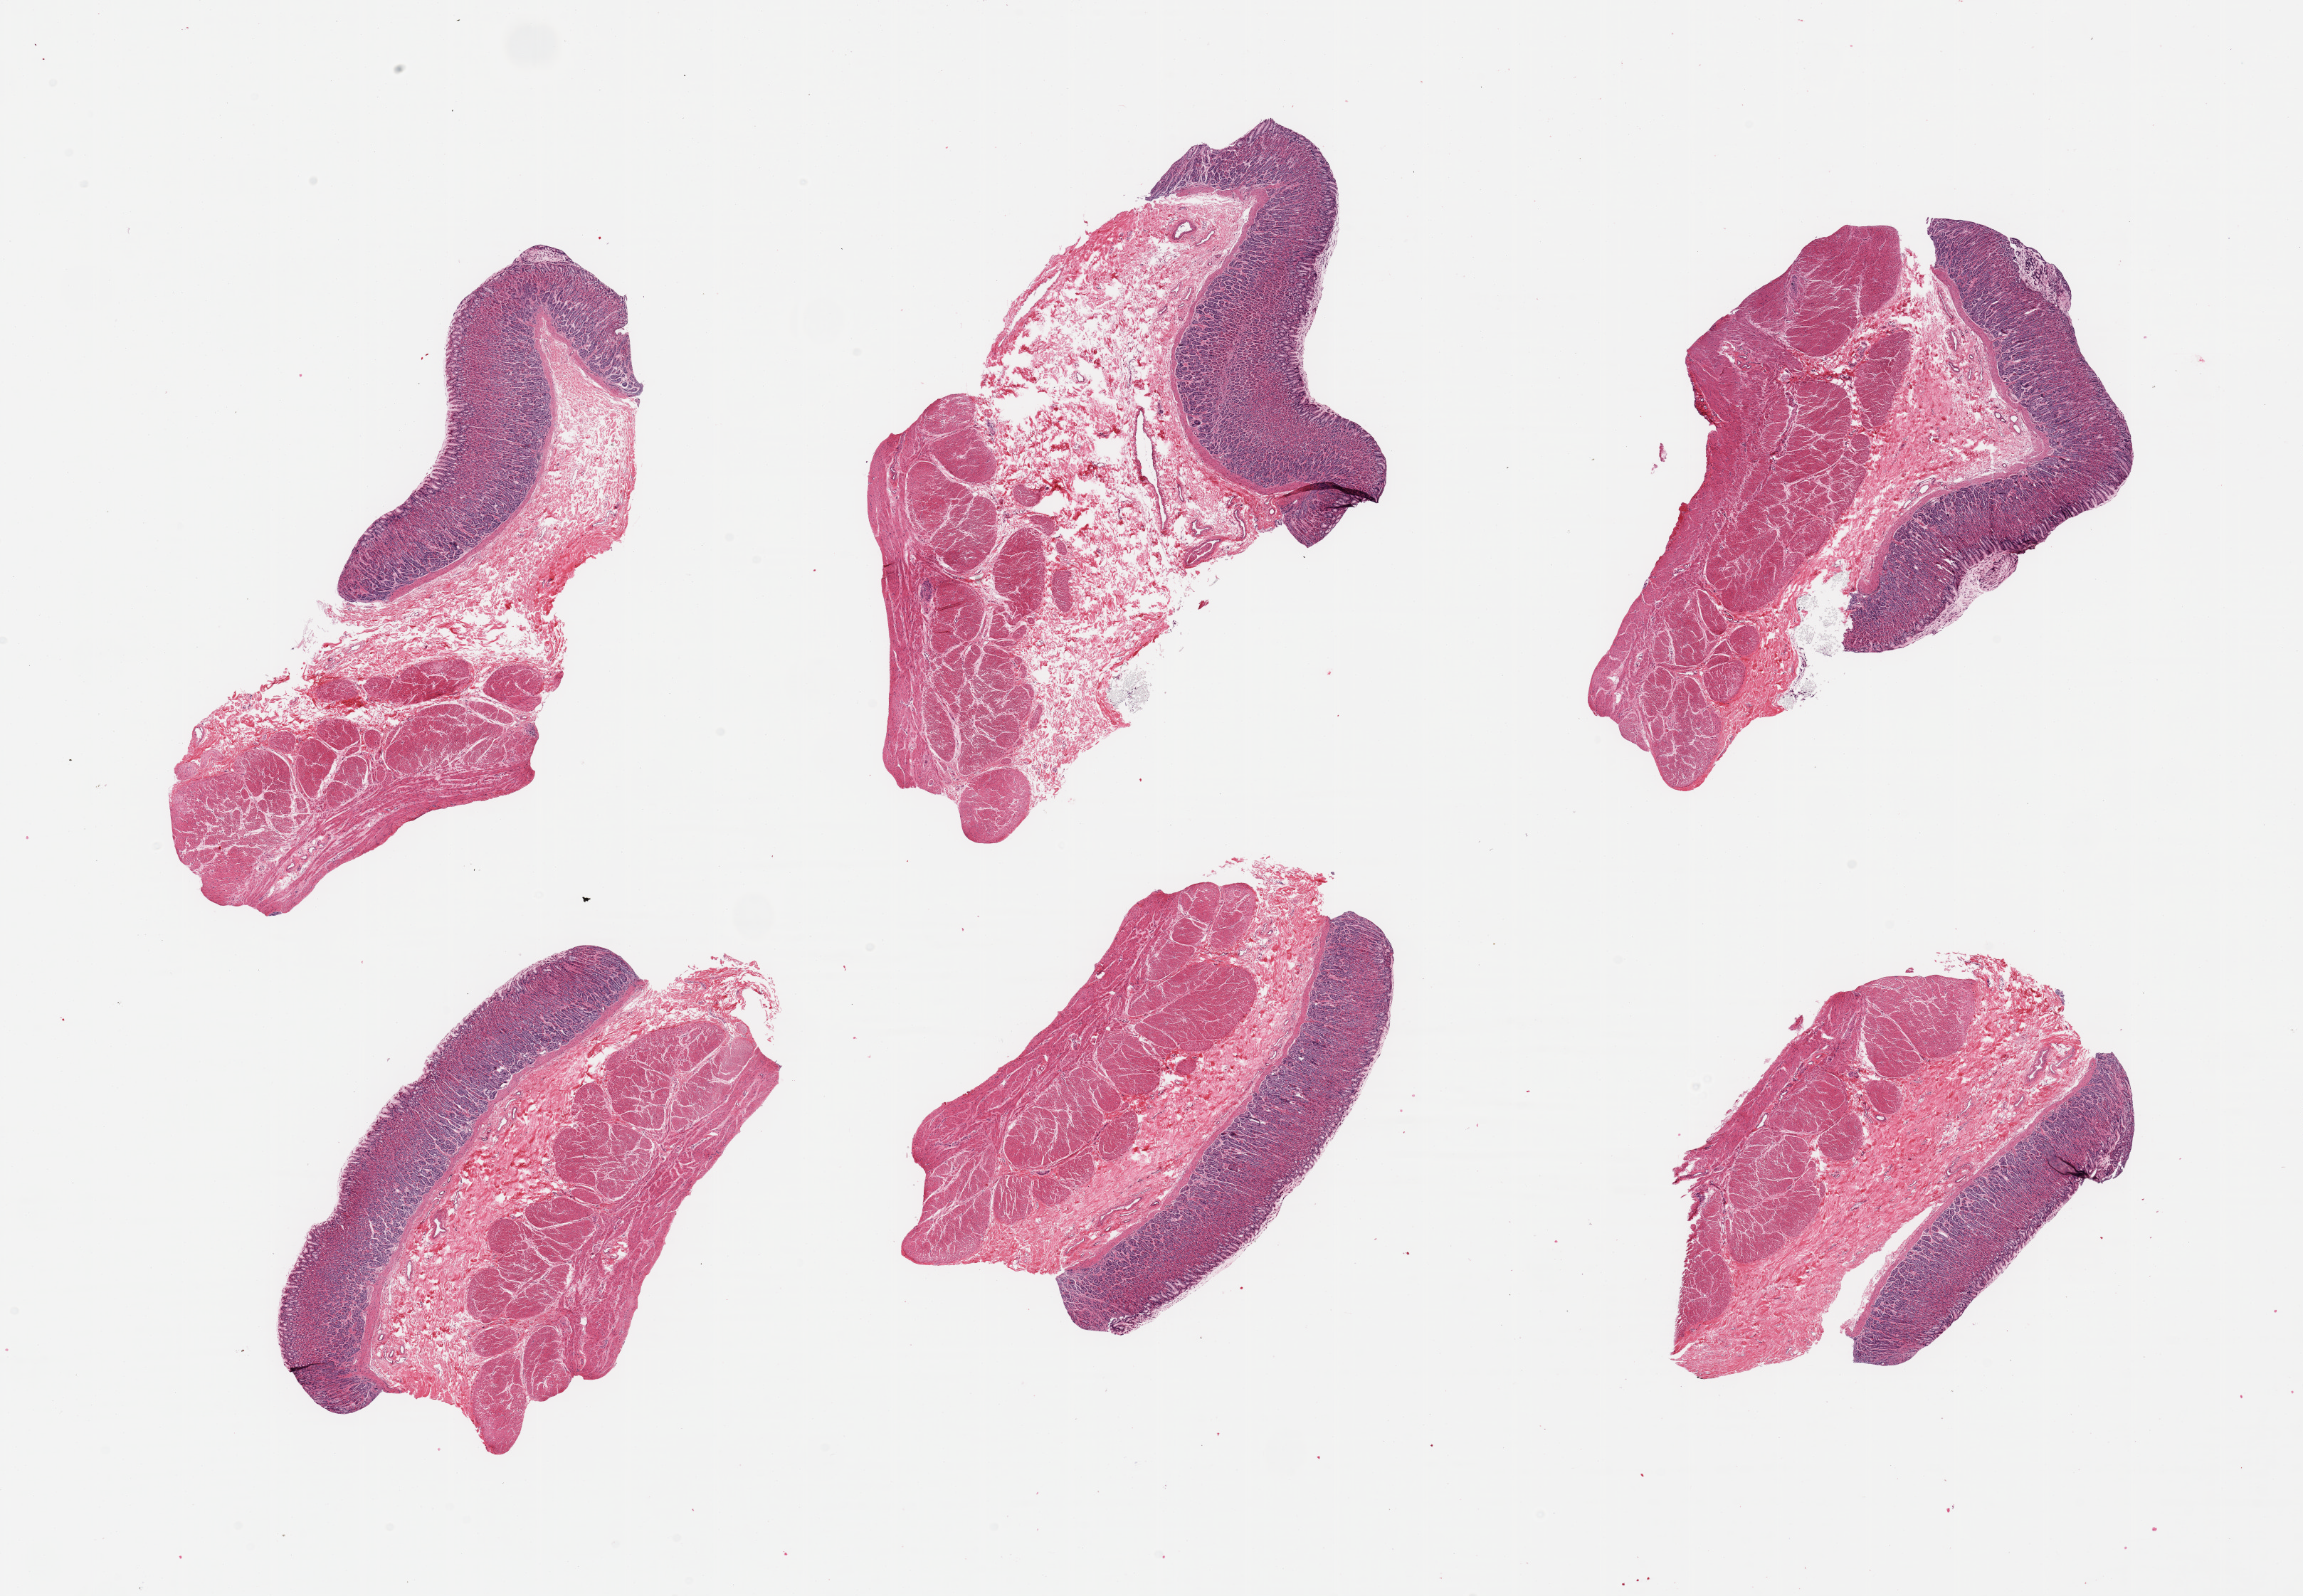
Digitized hematoxylin and eosin (H&E)-stained section — low-resolution overview of the scanned area, about 25.6 x 17.7 mm. PAXgene-fixed paraffin-embedded (PFPE) section. Section of stomach (target tissue). Donor tissue sample. Male donor.
Reviewer comment on this tissue sample: 6 pieces; full thickness sections.